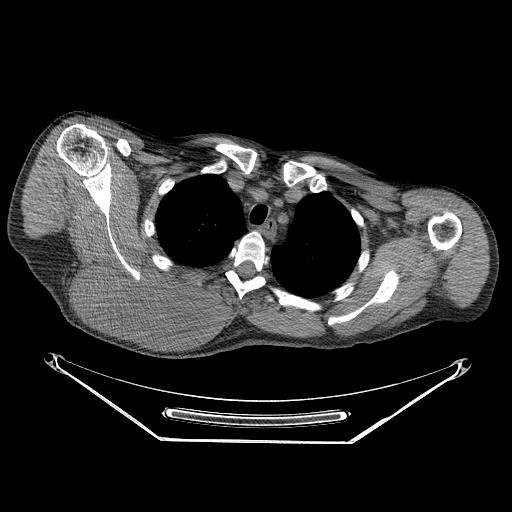
CT of an extremity soft-tissue mass (from a PET/CT study), one axial slice. Position 194 of 267 along the scan axis. Reconstruction kernel STANDARD. 140 kVp. Soft-tissue window (W 400 / L 40 HU). 3.75 mm slice thickness. 512 × 512 image matrix, field of view 500 × 500 mm. Male patient. From the clinical record (not read from this slice): histological type: pleiomorphic spindle cell undifferentiated; grade: high; site of the primary tumour: right parascapusular.
Structures marked on this image (expert contour drawn on MRI and transferred to this co-registered scan by the dataset authors):
- gross tumour volume including surrounding oedema: bounding box <77,262,232,337> (left, top, right, bottom; pixels)
- gross tumour volume (mass): <77,262,216,336>